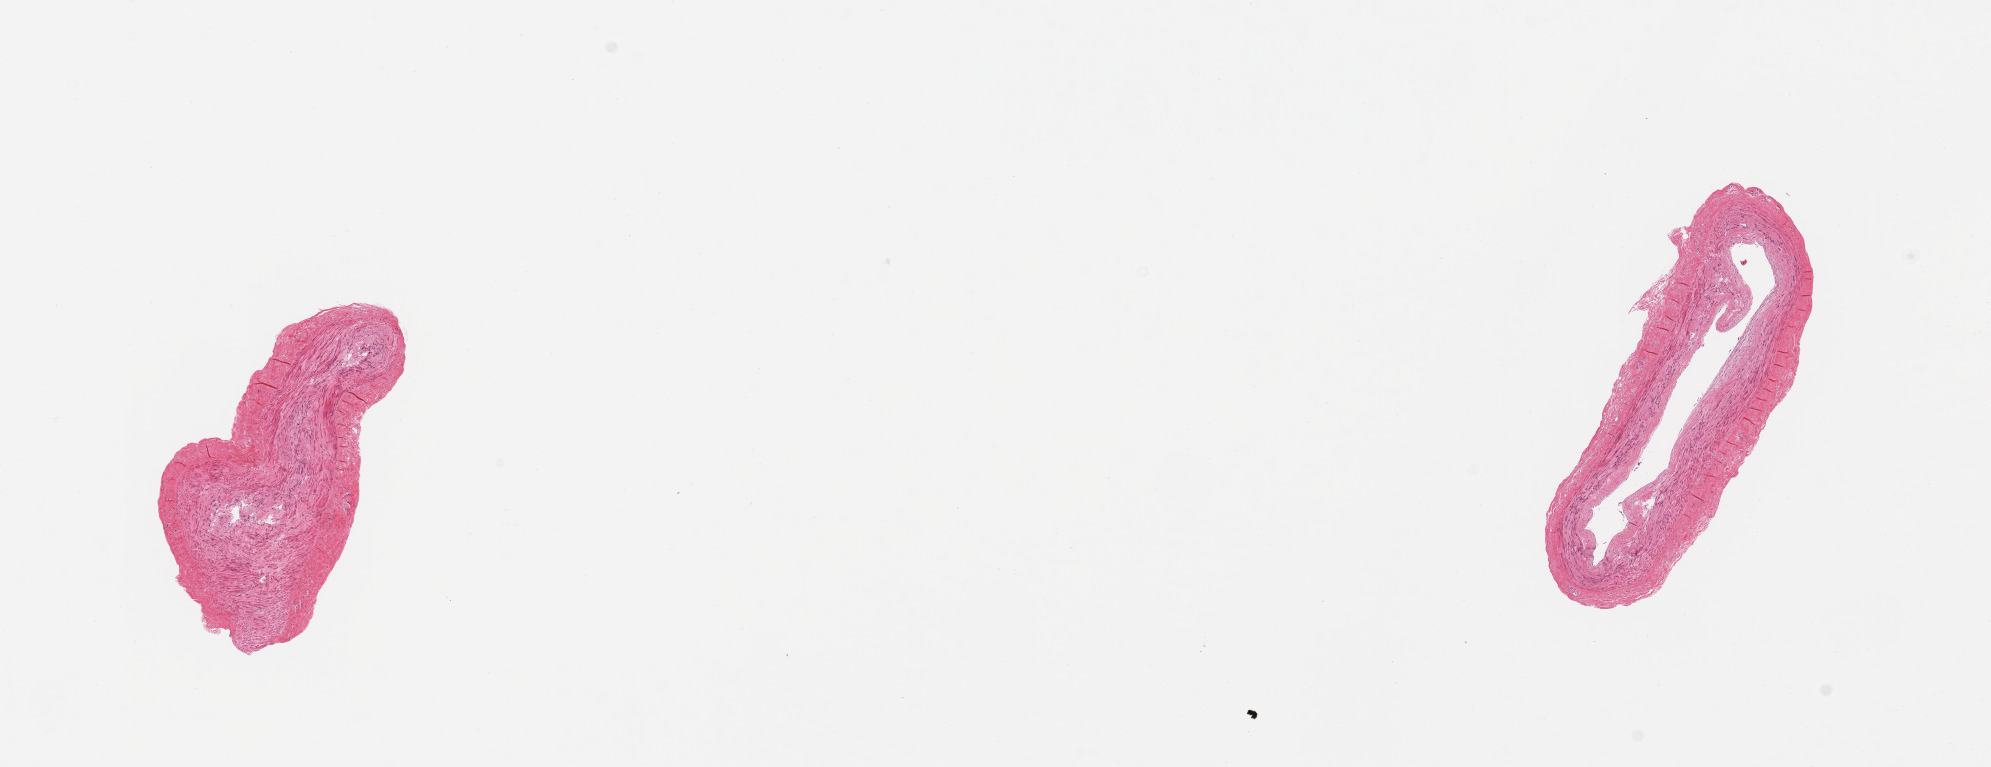
H&E whole-slide image — a low-resolution overview of the entire scanned area, about 15.8 x 6.1 mm (acquisition: 20x scan), PAXgene-fixed, paraffin-embedded tissue, target tissue: tibial artery, donor tissue sample. Male donor.
Review note (as recorded): 2 pieces; well trimmed; fibrous plaques.